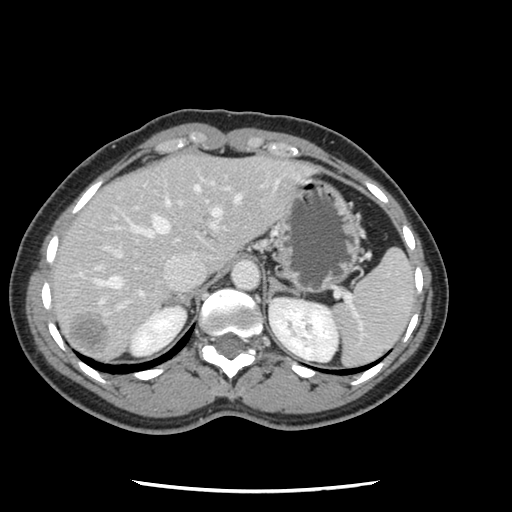
Contrast-enhanced abdominal CT, one axial slice. Position 89 of 134 along the scan axis. Intravenous contrast given. Soft-tissue window (W 400 / L 40 HU). 2.5 mm slice thickness. 512 × 512 image matrix, field of view 330 × 330 mm. Female patient, age 43 years. From the clinical record (not read from this slice): diagnosis: colorectal cancer liver metastases, imaged before liver resection; multiple liver metastases: yes; largest metastasis: 3.4 cm; chemotherapy before resection: no.
Structures marked on this image (expert manual segmentation):
- hepatic veins: bounding box (x1, y1, x2, y2) in pixels: (94, 185, 240, 303)
- liver: (53, 154, 311, 362)
- planned liver remnant (the part of the liver to remain after resection): (53, 158, 191, 309)
- portal vein (with intrahepatic branches): (71, 181, 230, 317)
- liver metastasis: (71, 314, 108, 351)